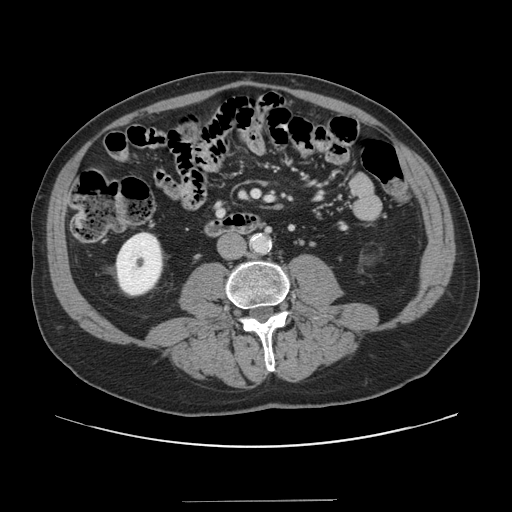
Contrast-enhanced abdominal CT, one axial slice; position 23 of 151 along the scan axis; 120 kVp; intravenous contrast given; soft-tissue window (W 400 / L 40 HU); 2.5 mm slice thickness; 512 × 512 image matrix, field of view 399 × 399 mm. Male patient, age 63 years. Case-level facts recorded for this patient, not image findings: diagnosis: colorectal cancer liver metastases, imaged before liver resection; multiple liver metastases: no.
Annotated regions visible in this slice (manually delineated by an expert):
- portal vein (with intrahepatic branches): bounding box [x1, y1, x2, y2] px = [253, 191, 270, 199]